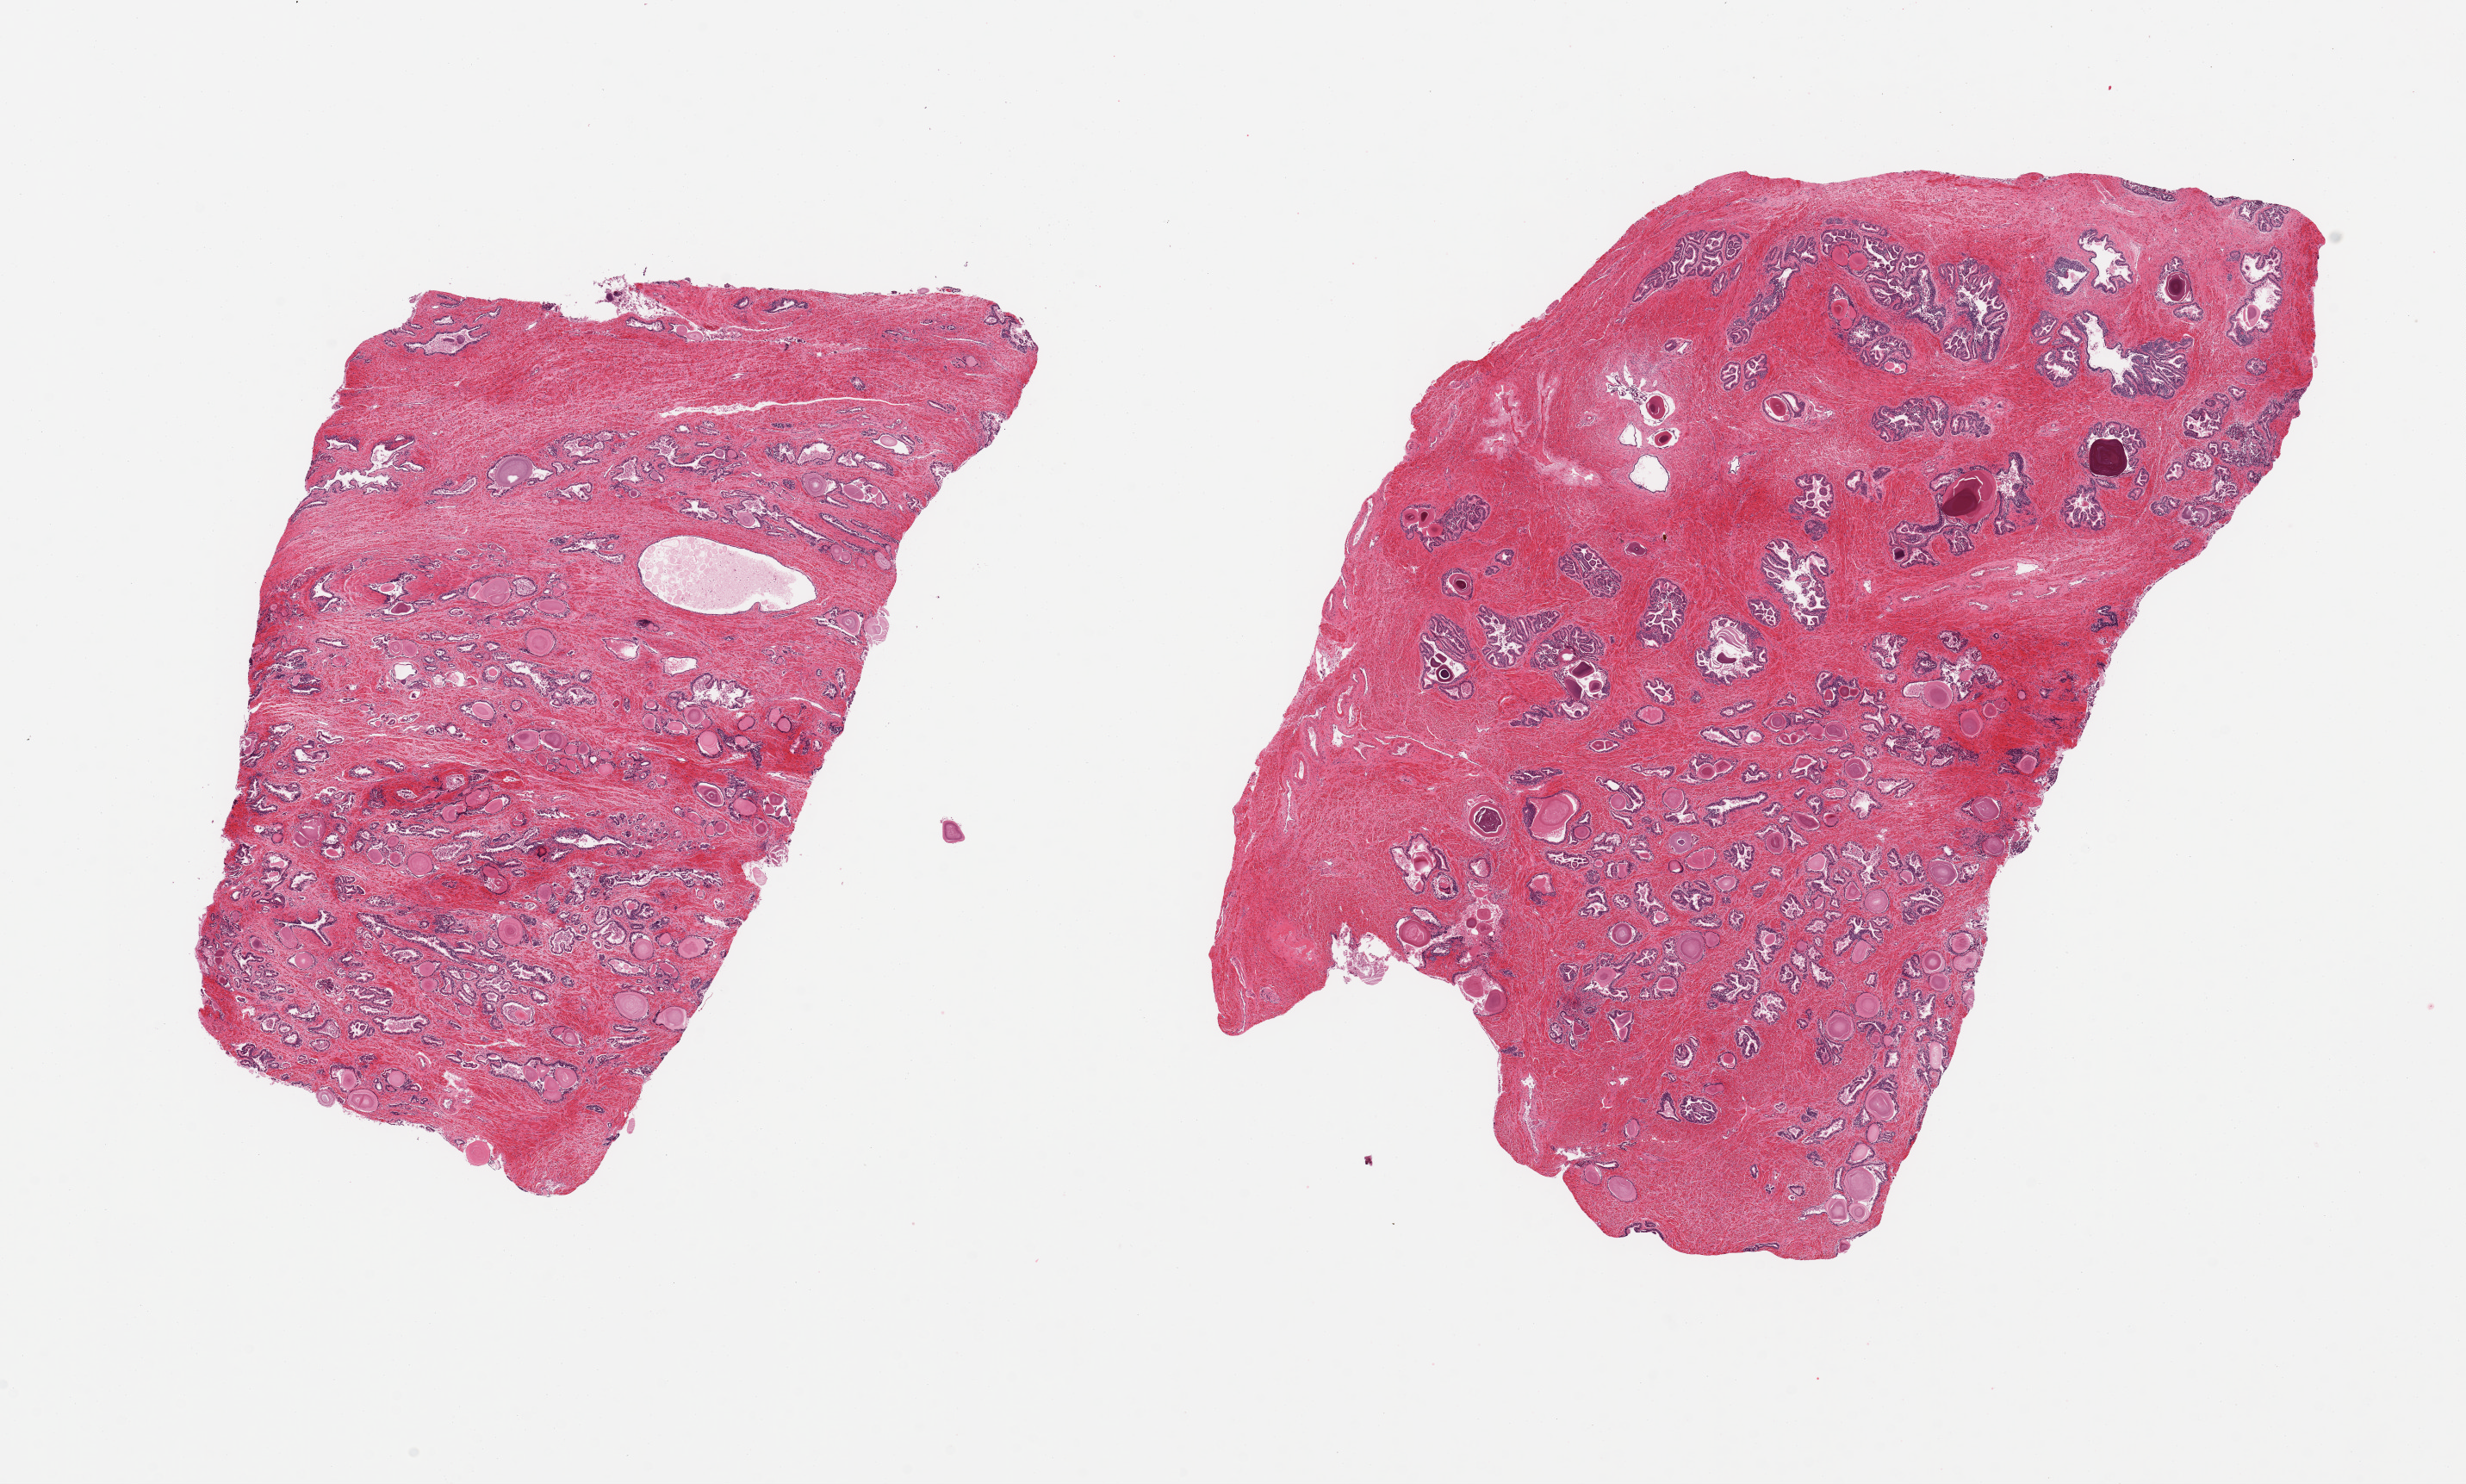
Digitized hematoxylin and eosin (H&E)-stained section, brightfield, shown as a low-resolution overview of the whole scanned area (about 22.6 x 13.6 mm, slide scanned at 20x). PAXgene-fixed paraffin-embedded (PFPE) section. Sampled site (target tissue): prostate. Donor tissue sample.
- review note (as recorded): 2 pieces; fibromuscular stroma with admixed glands, numerous corpora amylacea, some sloughing